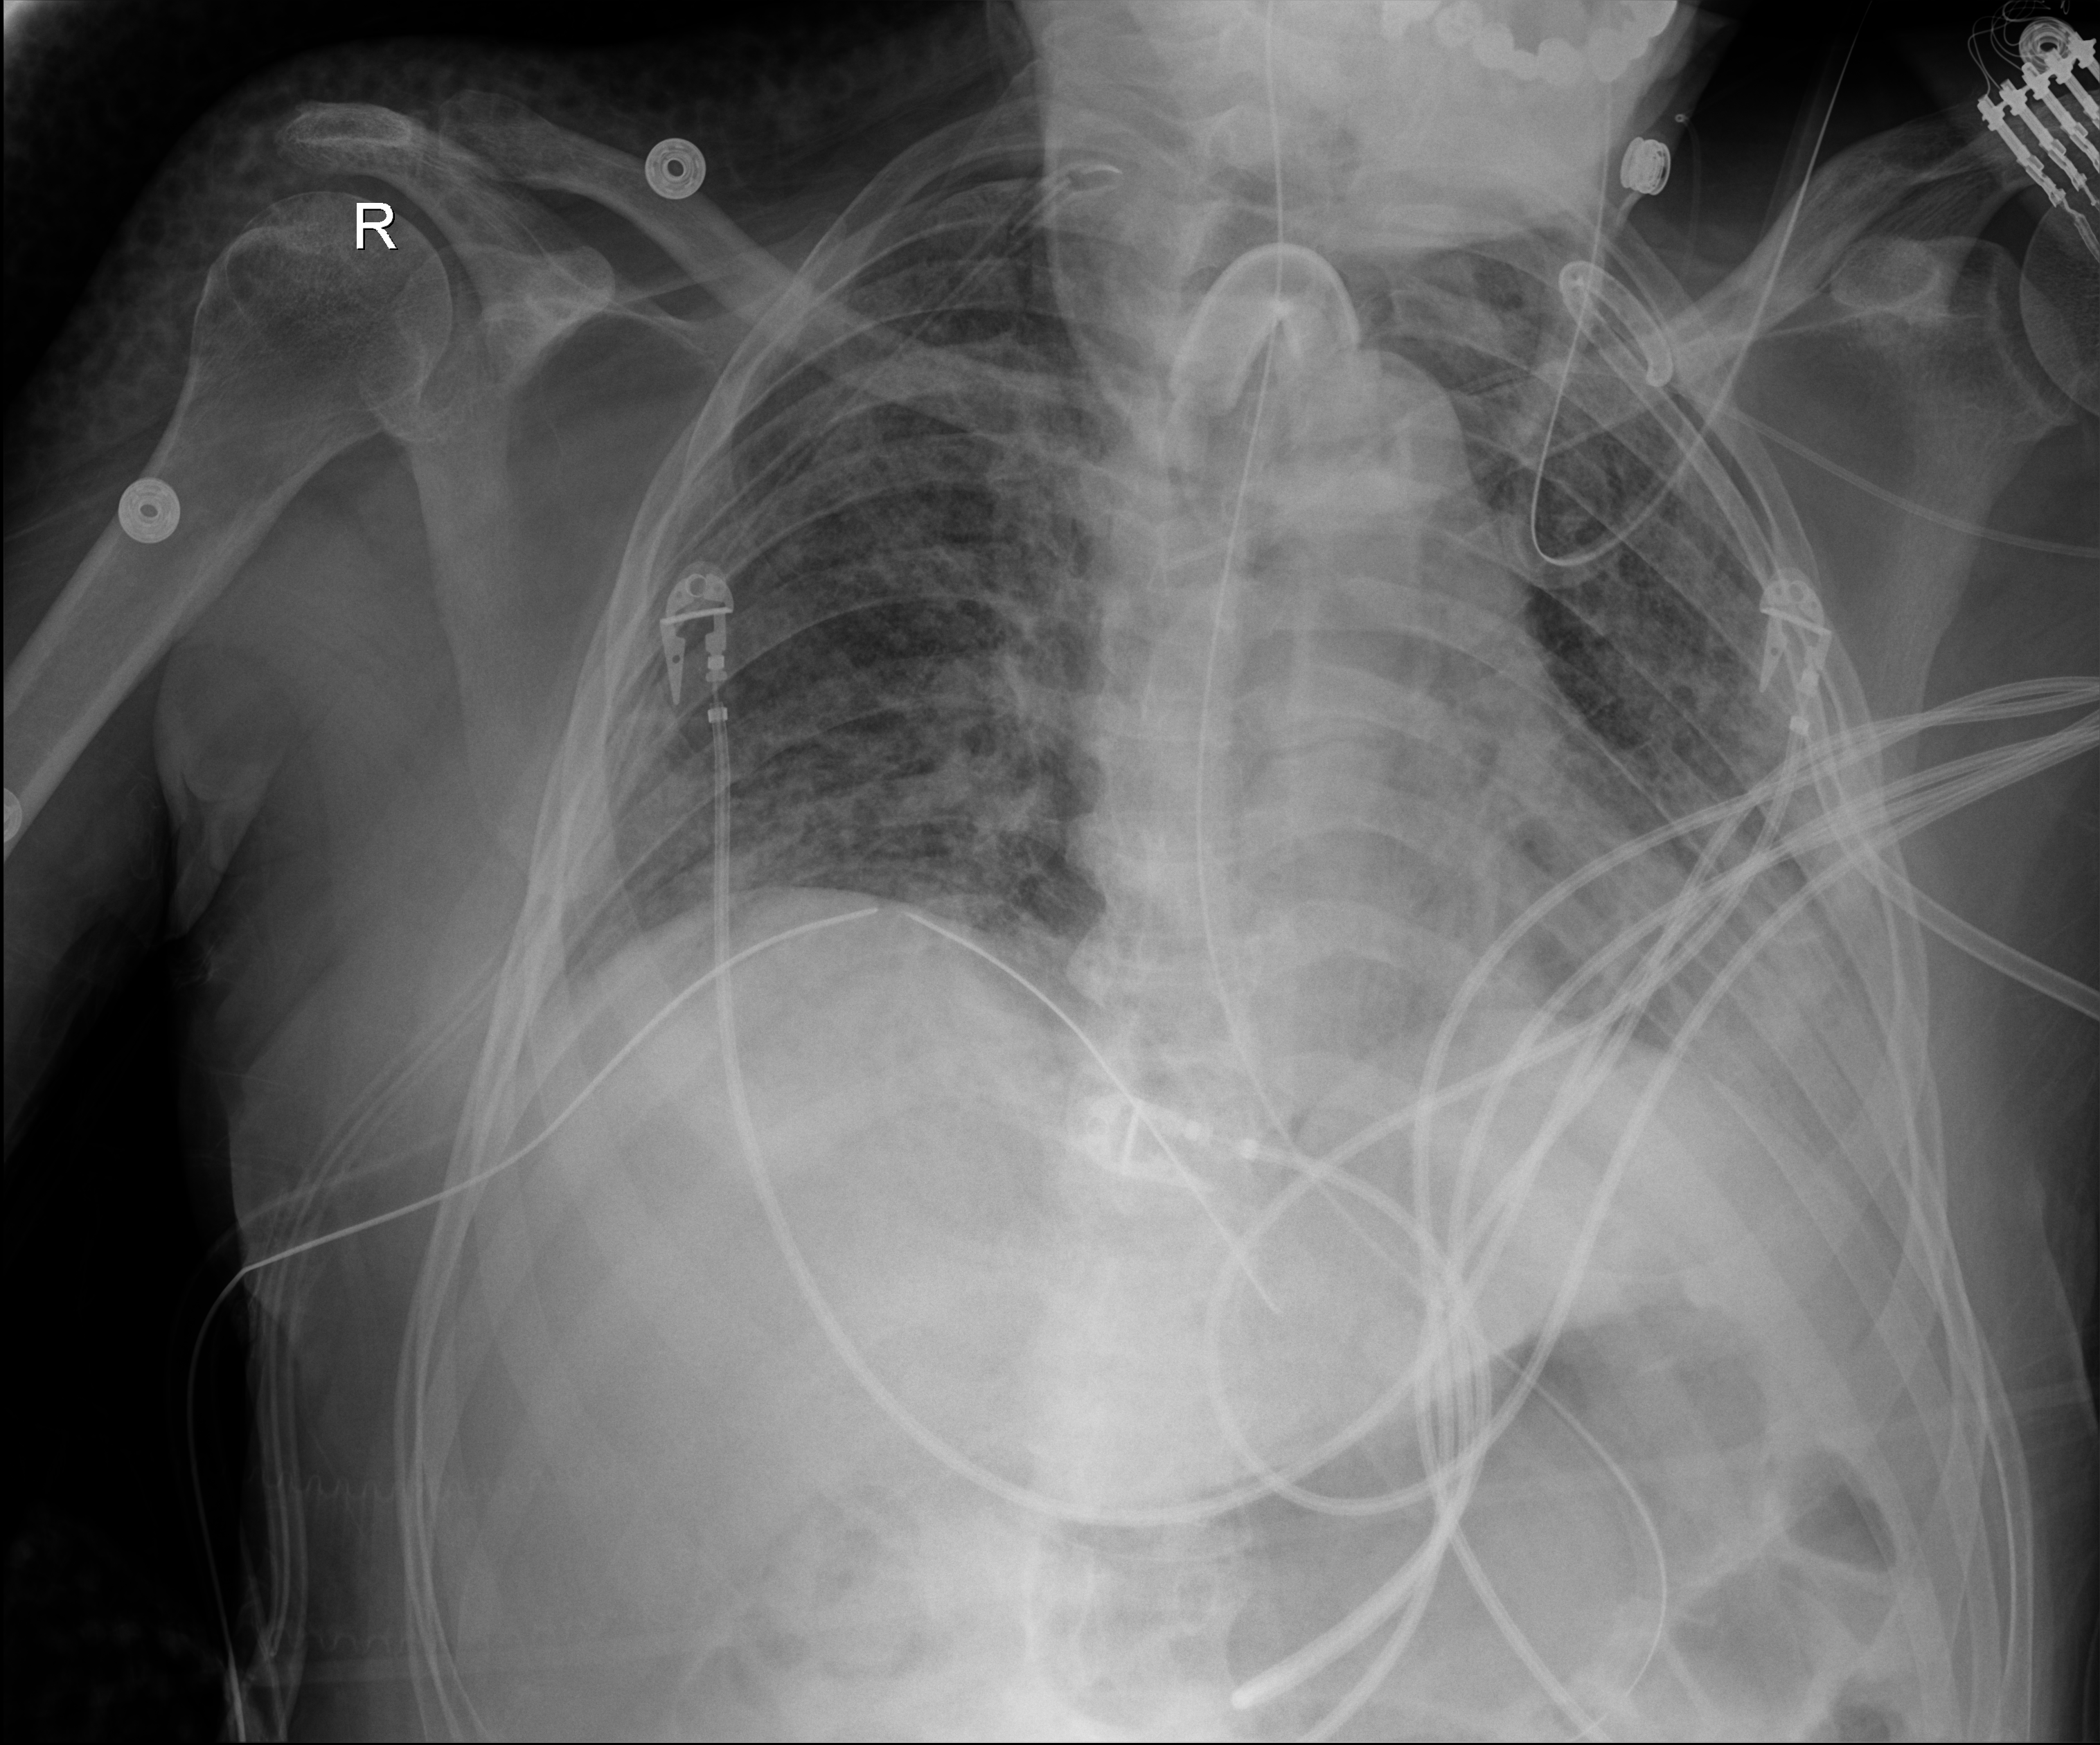
Chest X-ray (portable); anteroposterior (AP) projection. Patient hospitalised with COVID-19; male, aged 18–59 years.
From the hospital-stay record, not from the radiograph (when in the stay this image was taken is not recorded):
- mechanically ventilated during this hospital stay: yes